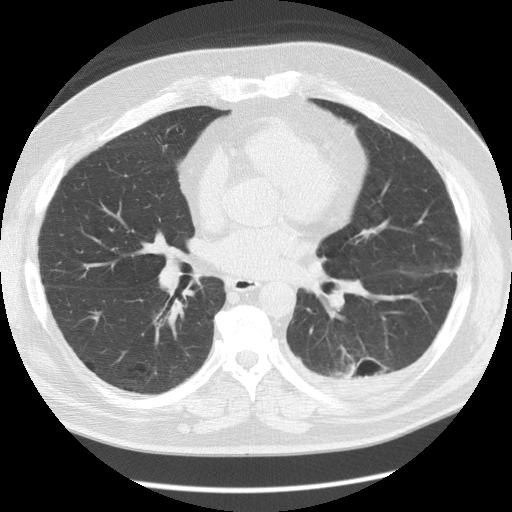
Axial slice from a low-dose chest CT screening exam; baseline screening round; lung window (W 1500 / L -600 HU); 2.5 mm slice thickness; standard (soft-tissue) reconstruction kernel (STANDARD); slice 63 of 126 in the series; 512 × 512 image matrix. Male, age 56 years at enrolment. Former smoker at enrolment.
• Expert reader's lesion annotation, bounding box [x1, y1, x2, y2] px = [325, 344, 398, 396].
• The screening reader recorded 4 non-calcified nodules or masses ≥4 mm on this exam; which of them this box marks is not recorded.
• Official screen result: positive, change unspecified: nodule(s) >= 4 mm or enlarging nodule(s), mass(es), or other non-specific abnormalities suspicious for lung cancer.
• Participant outcome: lung cancer diagnosed 173 days after this screen — non-small cell carcinoma, left lower lobe, stage IV (AJCC 6th edition), 50 mm at pathology.